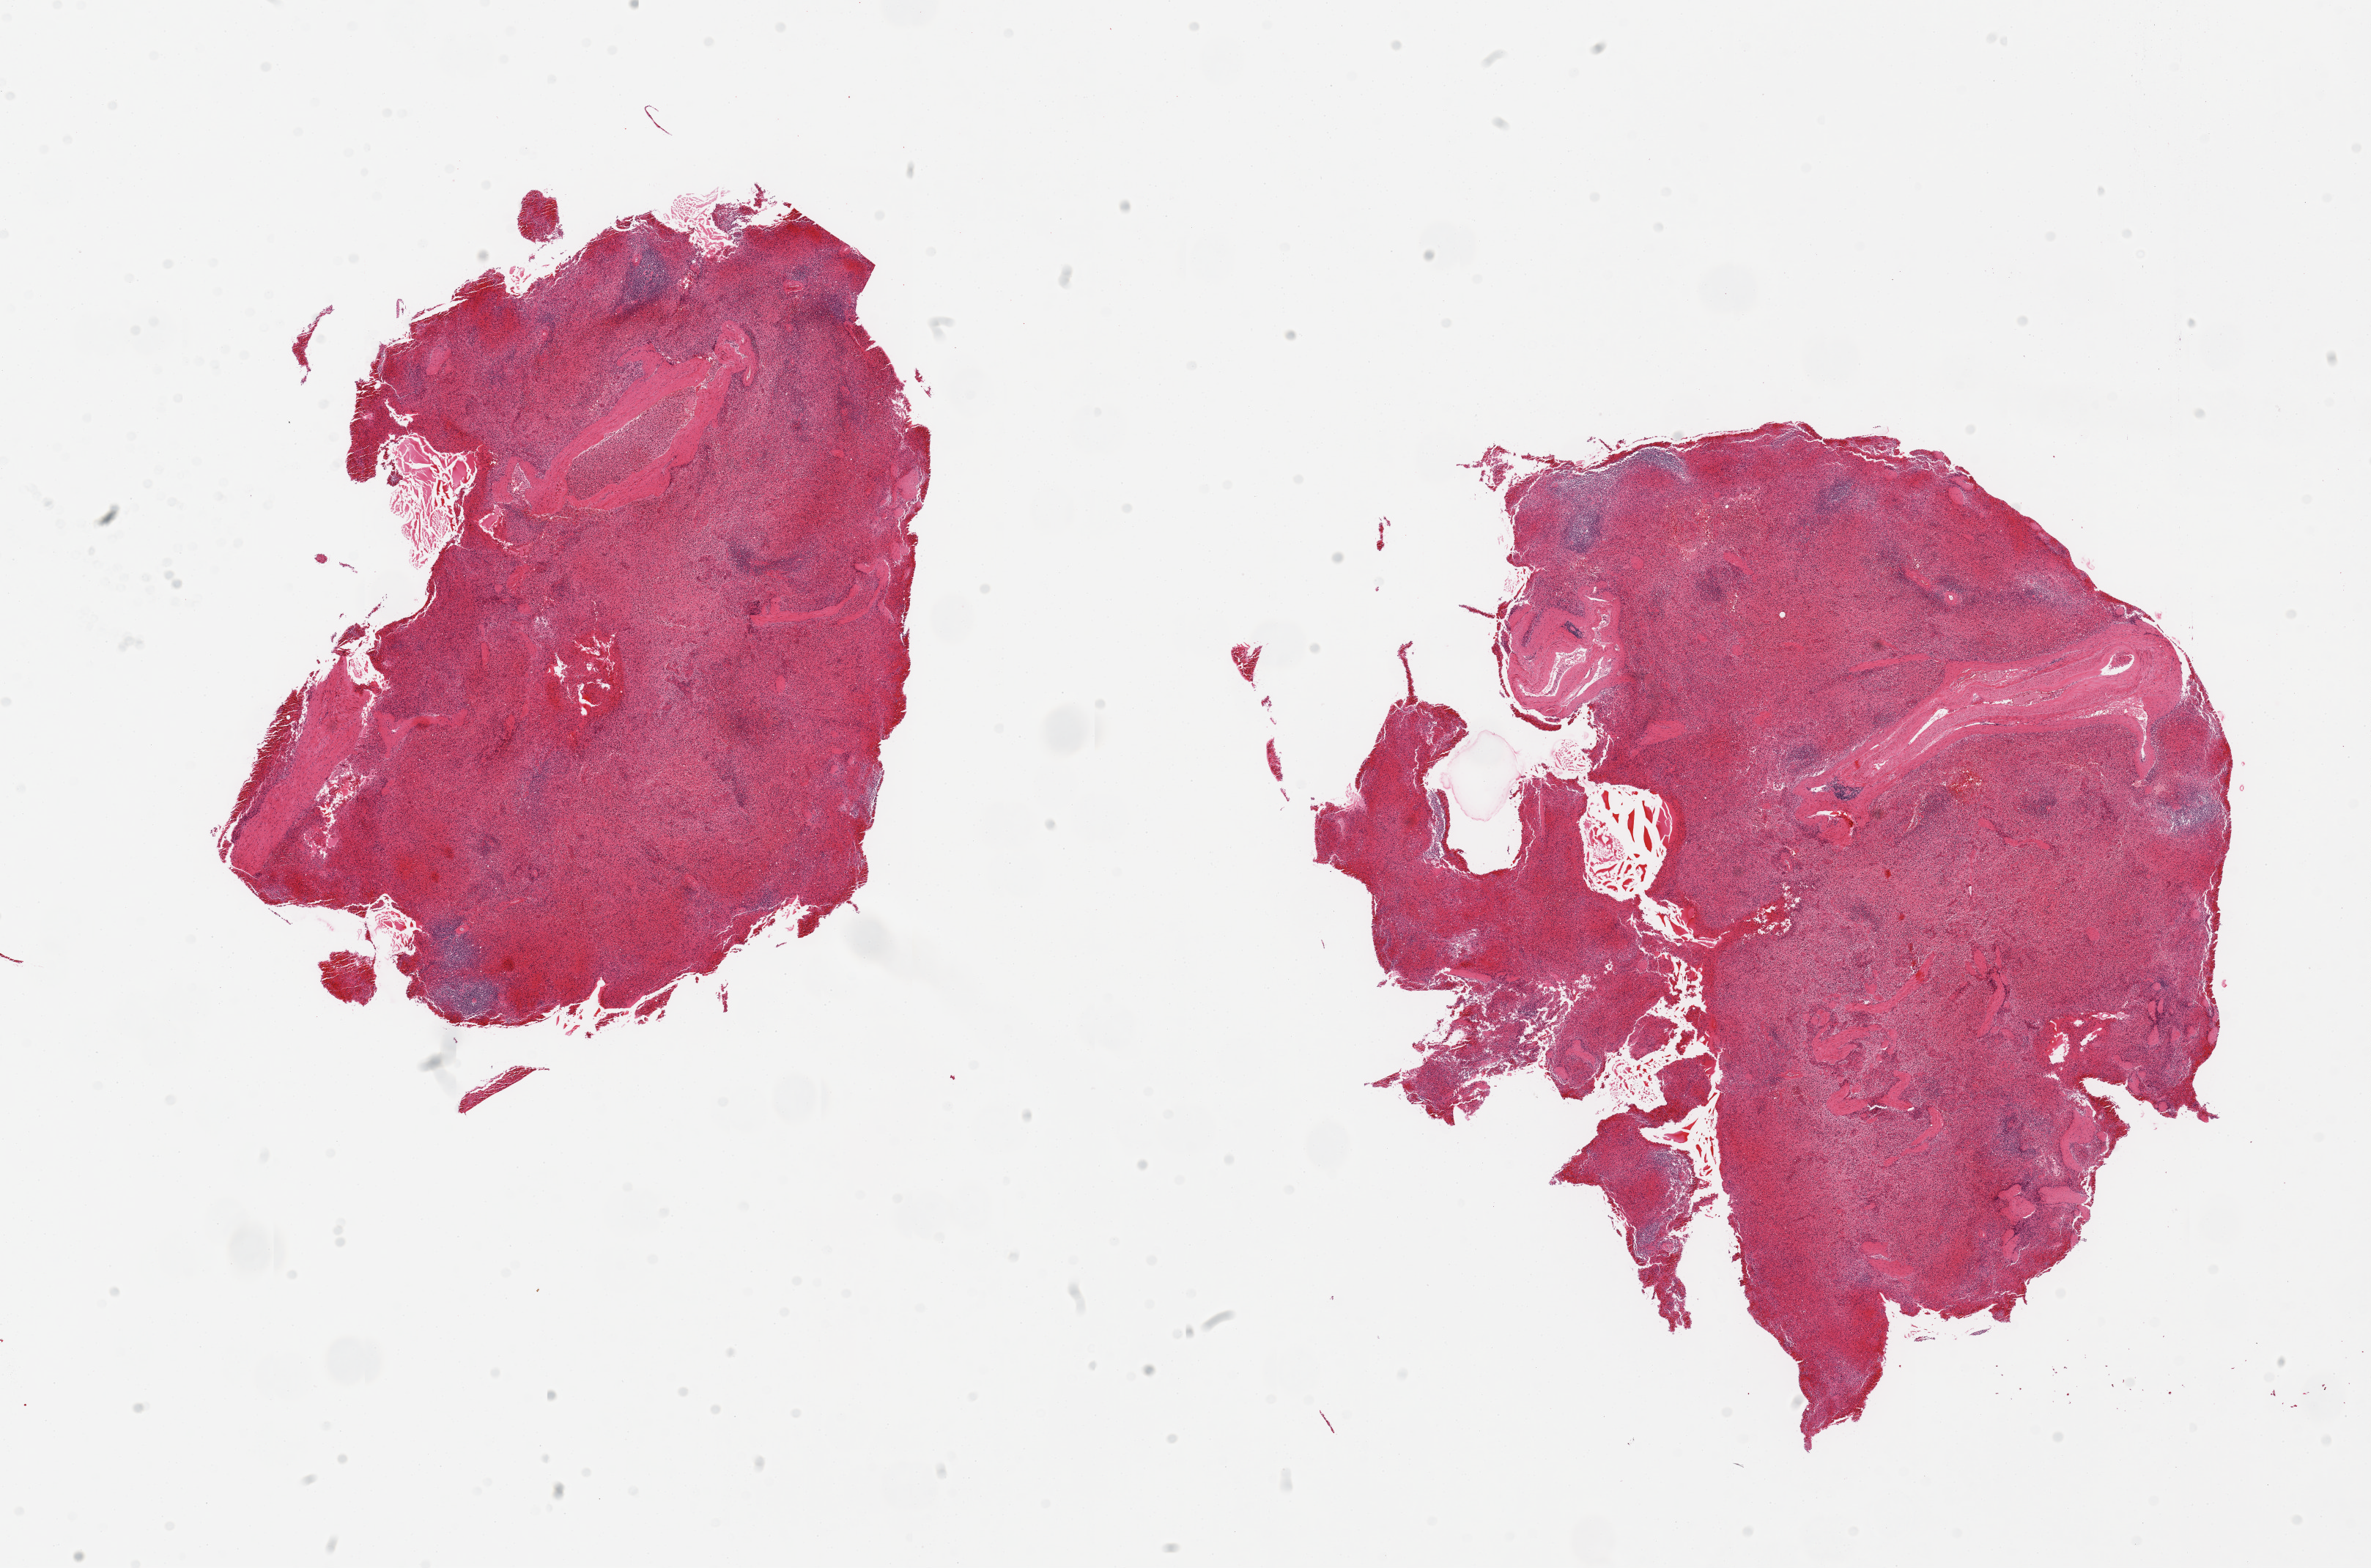
Whole-slide image, haematoxylin and eosin stain, low-resolution overview of the scanned area, about 25.6 x 16.9 mm (acquisition: 20x scan). PAXgene-fixed paraffin-embedded (PFPE) section. Target tissue: spleen. Donor tissue sample. Male donor.
Pathologist's review note for this sample: 2 pieces, moderate-marked congesion and autolysis.